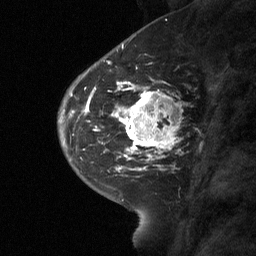
Breast MRI (dynamic contrast-enhanced), one sagittal slice; position 24 of 64 along the scan axis; dynamic contrast-enhanced study with each time point stored as its own series, time point 2 of 3 at this slice position (early post-contrast, ordered by acquisition time); 1.5 T; TE 4.8 ms, TR 27 ms; 256 × 256 image matrix, field of view 180 × 180 mm. Patient: female, 42 years. From the clinical record (not read from this slice): setting: breast cancer imaged before/during neoadjuvant chemotherapy; receptor status: triple-negative.
Structures marked on this image (semi-automatically segmented with operator editing):
- analysis volume of interest (the breast-tissue region the enhancement analysis was run in; not a lesion): bounding box (x1, y1, x2, y2) in pixels: (115, 85, 180, 160)
- tumour enhancement mask (voxels above the 90 % enhancement threshold inside the analysis volume of interest): (115, 85, 176, 160)